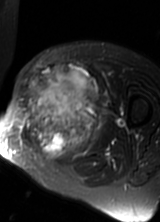
MRI of an extremity soft-tissue mass, one axial slice; slice 38 of 69 in the series (ordered by position); T2-weighted fat-saturated; MR volume resampled by the dataset authors to the PET/CT grid (not the native acquisition matrix); 3.27 mm slice thickness; 160 × 222 image matrix. Female patient. From the clinical record (not read from this slice): histological type: pleomorphic leiomyosarcoma; grade: high; site of the primary tumour: left thigh.
Structures marked on this image (expert contour drawn on MRI and transferred to this co-registered scan by the dataset authors):
- gross tumour volume including surrounding oedema: bounding box (x1, y1, x2, y2) in pixels: (22, 65, 103, 162)
- gross tumour volume (mass): (23, 65, 99, 158)